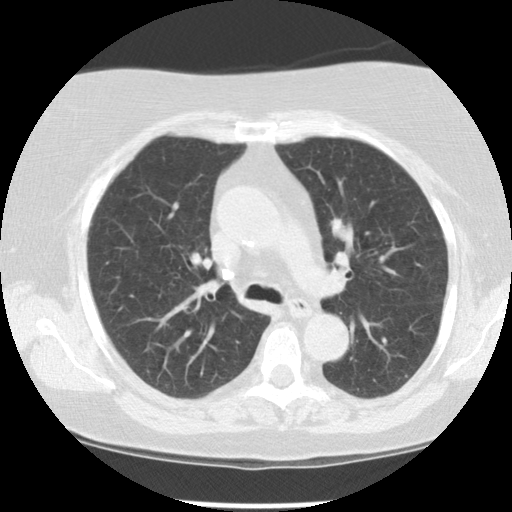
Chest CT (low-dose screening protocol), one axial image; first (baseline) screen; lung window (W 1500 / L -600 HU); standard (soft-tissue) reconstruction kernel (STANDARD); slice 35 of 108 in the series. Female, age 67 years at enrolment. Former smoker at enrolment.
- Expert-annotated lung lesion, bounding box <310,206,364,255> (left, top, right, bottom; pixels).
- The exam's reader record, not a measurement of the box and not confirmed to be the same lesion: non-calcified nodule or mass ≥4 mm, left upper lobe, 13 × 10 mm, poorly defined margins, soft tissue attenuation.
- Later outcome: lung cancer diagnosed 399 days after this screen (after the second annual screen) — adenocarcinoma, NOS, left upper lobe, moderately differentiated (G2), stage IIA (AJCC 6th edition), 23 mm at pathology.